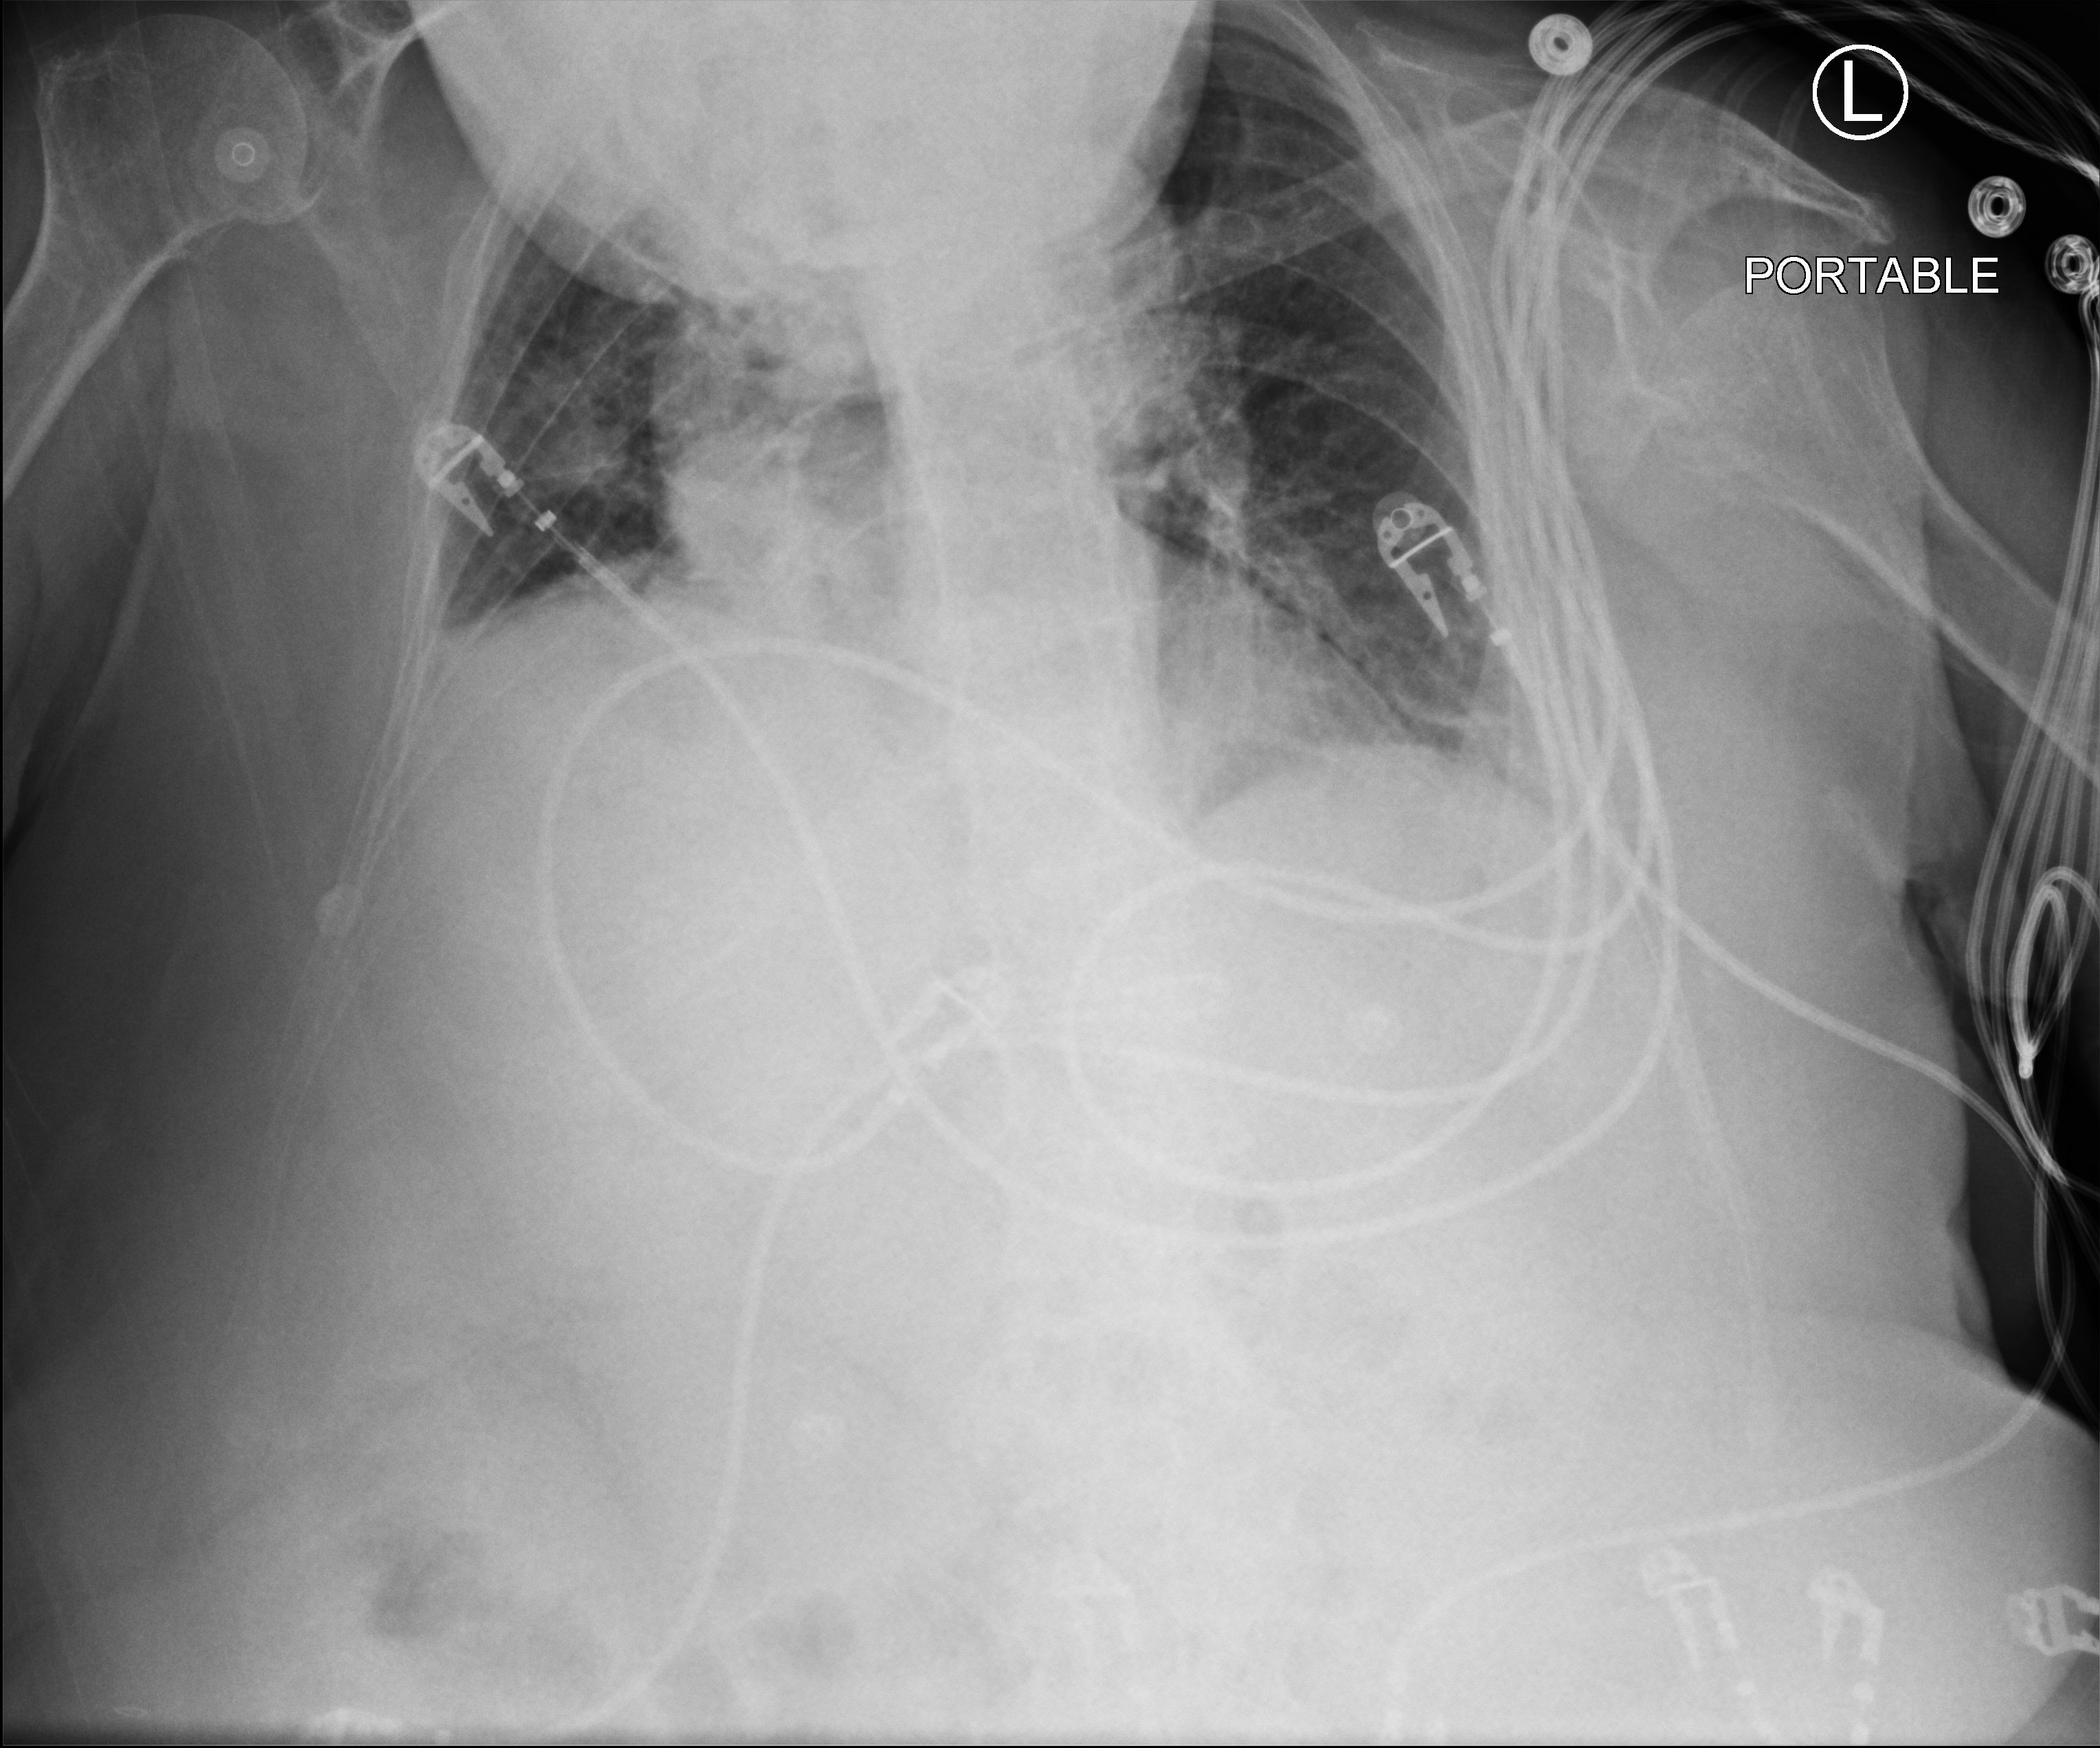
Bedside chest radiograph (computed radiography), anteroposterior (AP) projection. Female patient hospitalised with COVID-19, age 75–90 years.
From the hospital-stay record, not from the radiograph (when in the stay this image was taken is not recorded):
- length of hospital stay: 14 days